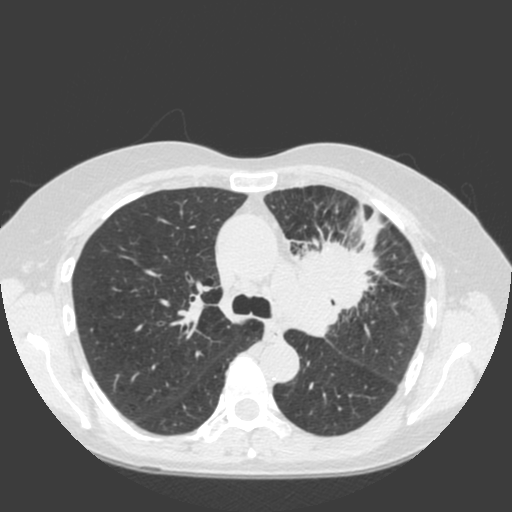
Low-dose screening chest CT, axial slice, baseline screening round, lung window (W 1500 / L -600 HU), 2 mm slice thickness, slice 58 of 184 in the series. Female, age 66 years at enrolment.
Expert reader's lesion annotation, bounding box <282,225,399,330> (left, top, right, bottom; pixels). Reader record for this screening exam (exam-level; its link to the box is not recorded): non-calcified nodule or mass ≥4 mm, left upper lobe, 61 × 45 mm, spiculated (stellate) margins, soft tissue attenuation. Lung cancer was diagnosed 19 days after this screen: squamous cell carcinoma, keratinizing, NOS, left upper lobe, left hilum, mediastinum, left main stem bronchus, other location, poorly differentiated (G3), stage IIIB (AJCC 6th edition), 60 mm at pathology.